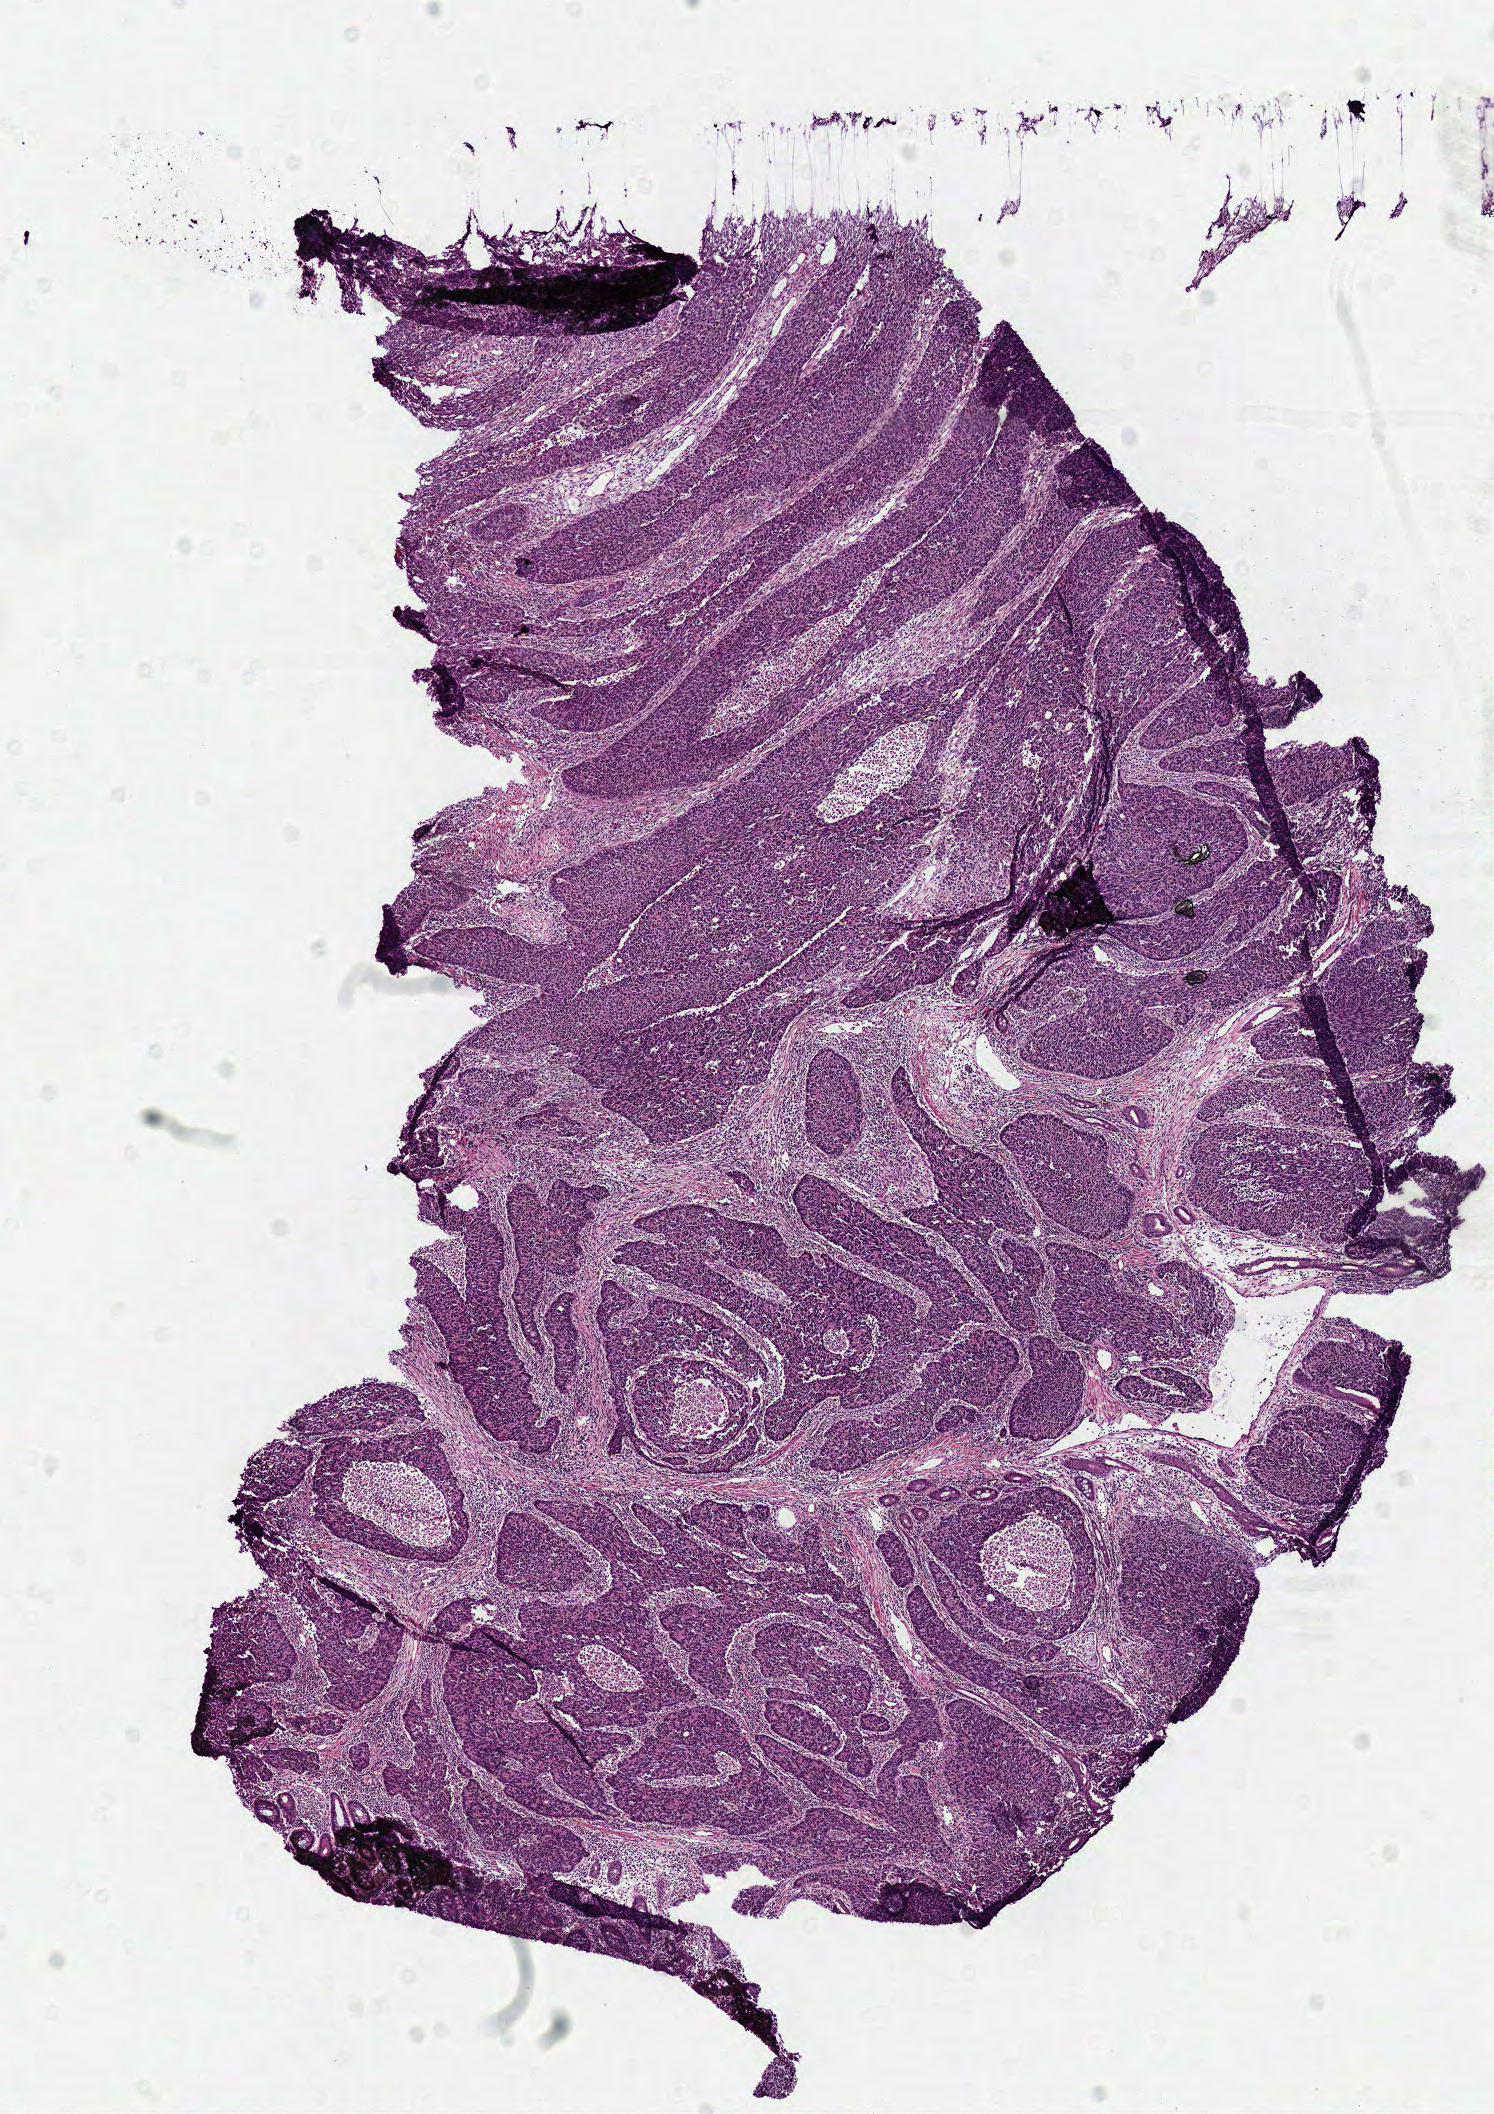
Whole-slide histology image, H&E, whole scanned area (about 5.9 x 8.3 mm, from a 40x scan) shown as a low-resolution overview. Frozen section from the top of the tissue portion. Primary tumour sample from the colon. Female patient; age at initial diagnosis 70 years.
Histologic diagnosis: Adenocarcinoma, NOS (cecum).